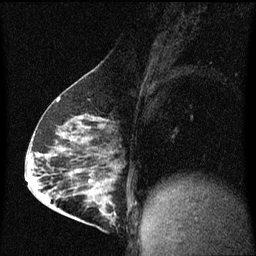
Breast MRI (dynamic contrast-enhanced), one sagittal slice; position 31 of 60 along the scan axis; dynamic contrast-enhanced series, image 2 of 3 at this slice position (ordered by acquisition); 1.5 T; TE 4.2 ms, TR 8 ms; 256 × 256 image matrix, field of view 200 × 200 mm. Patient: female, 63 years.
Structures marked on this image (semi-automatic segmentation, software-assisted and operator-edited):
- analysis volume of interest (the breast-tissue region the enhancement analysis was run in; not a lesion): bounding box (x1, y1, x2, y2) in pixels: (88, 182, 119, 229)
- tumour enhancement mask (voxels above the 70 % enhancement threshold inside the analysis volume of interest): (100, 194, 115, 221)